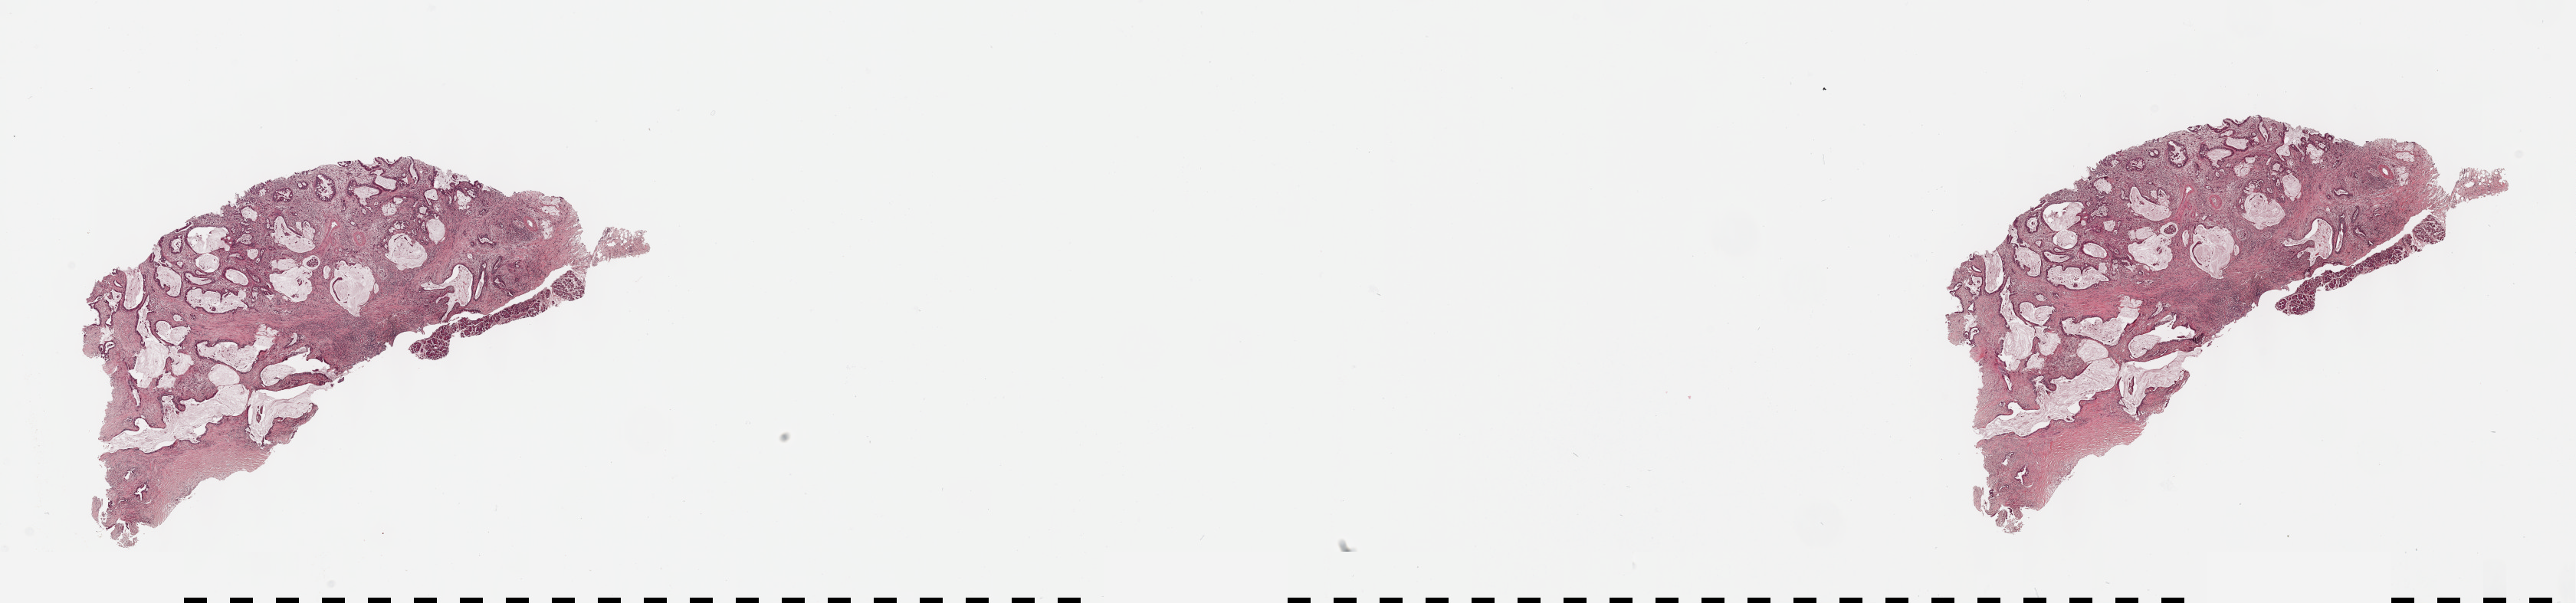
Whole-slide histology image, H&E, shown as a low-resolution overview of the whole scanned area (about 27.2 x 6.4 mm, acquisition: 40x scan). Formalin-fixed paraffin-embedded (FFPE) diagnostic section. Primary tumour sample from the pancreas. Female patient; age at initial diagnosis 65 years. Histologic grade: G1 (well differentiated).
AJCC pathologic stage: IIB (7th edition). Pathologic diagnosis: Infiltrating duct carcinoma, NOS (head of pancreas).